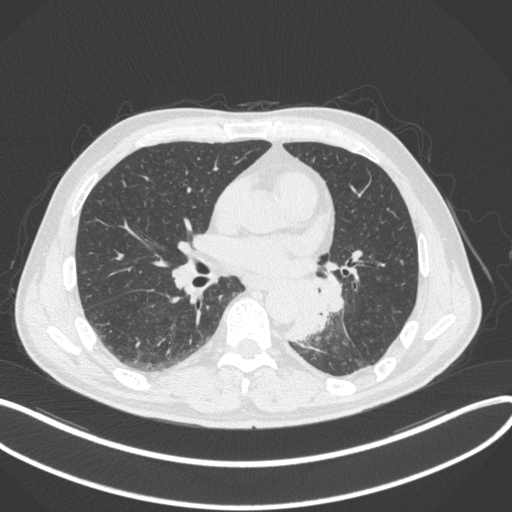
Chest CT, one axial slice. Slice 161 of 328 in the series (ordered by position). Reconstruction kernel B31f. 120 kVp. Lung window (W 1500 / L -600 HU). 1 mm slice thickness. 512 × 512 image matrix. Patient: male, 59 years. Case-level facts recorded for this patient, not image findings: clinical TNM (as recorded): T2a N2 M0.
Structures marked on this image (bounding box drawn by a radiologist):
- lung tumour (recorded histology: squamous cell carcinoma): box from (x=281, y=273) to (x=344, y=345) px